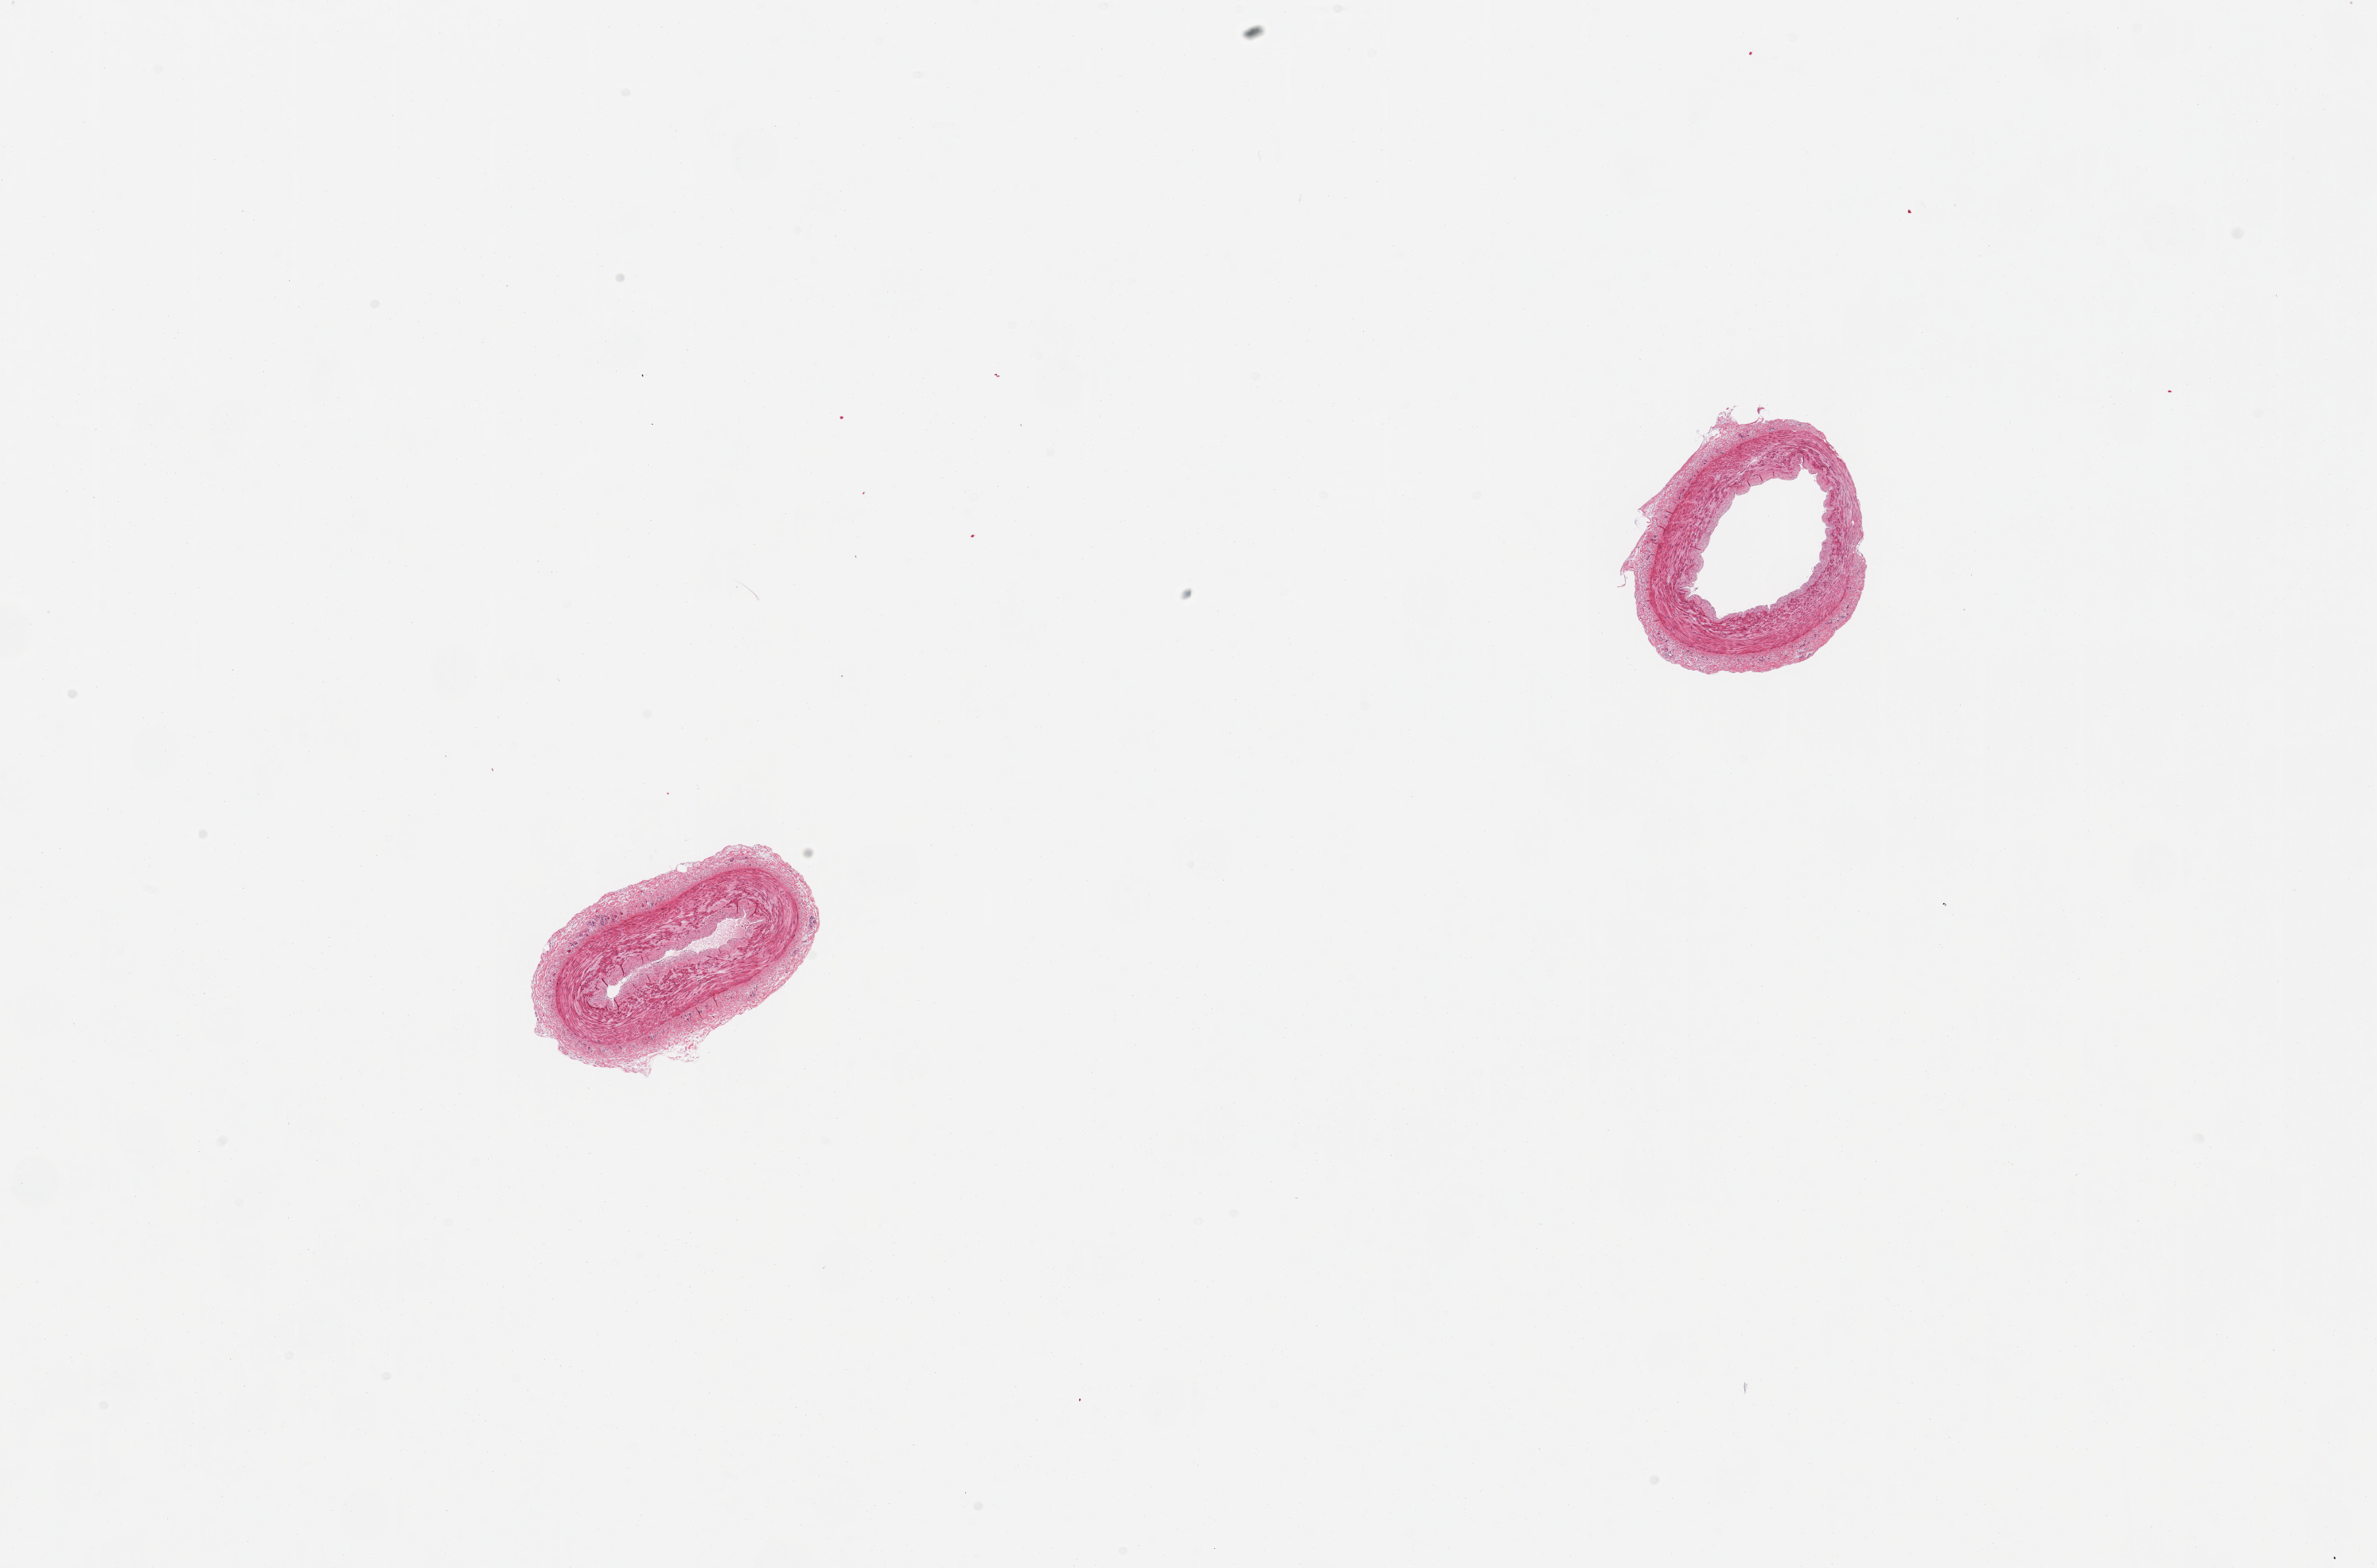
Digitized H&E-stained section, brightfield, a low-resolution overview of the entire scanned area, about 23.6 x 15.6 mm. PAXgene-fixed, paraffin-embedded tissue. Target tissue: tibial artery. Tissue donor sample. Donor sex: male.
* reviewer comment on this tissue sample: 2 pieces; no adherent fat or significant atherosis